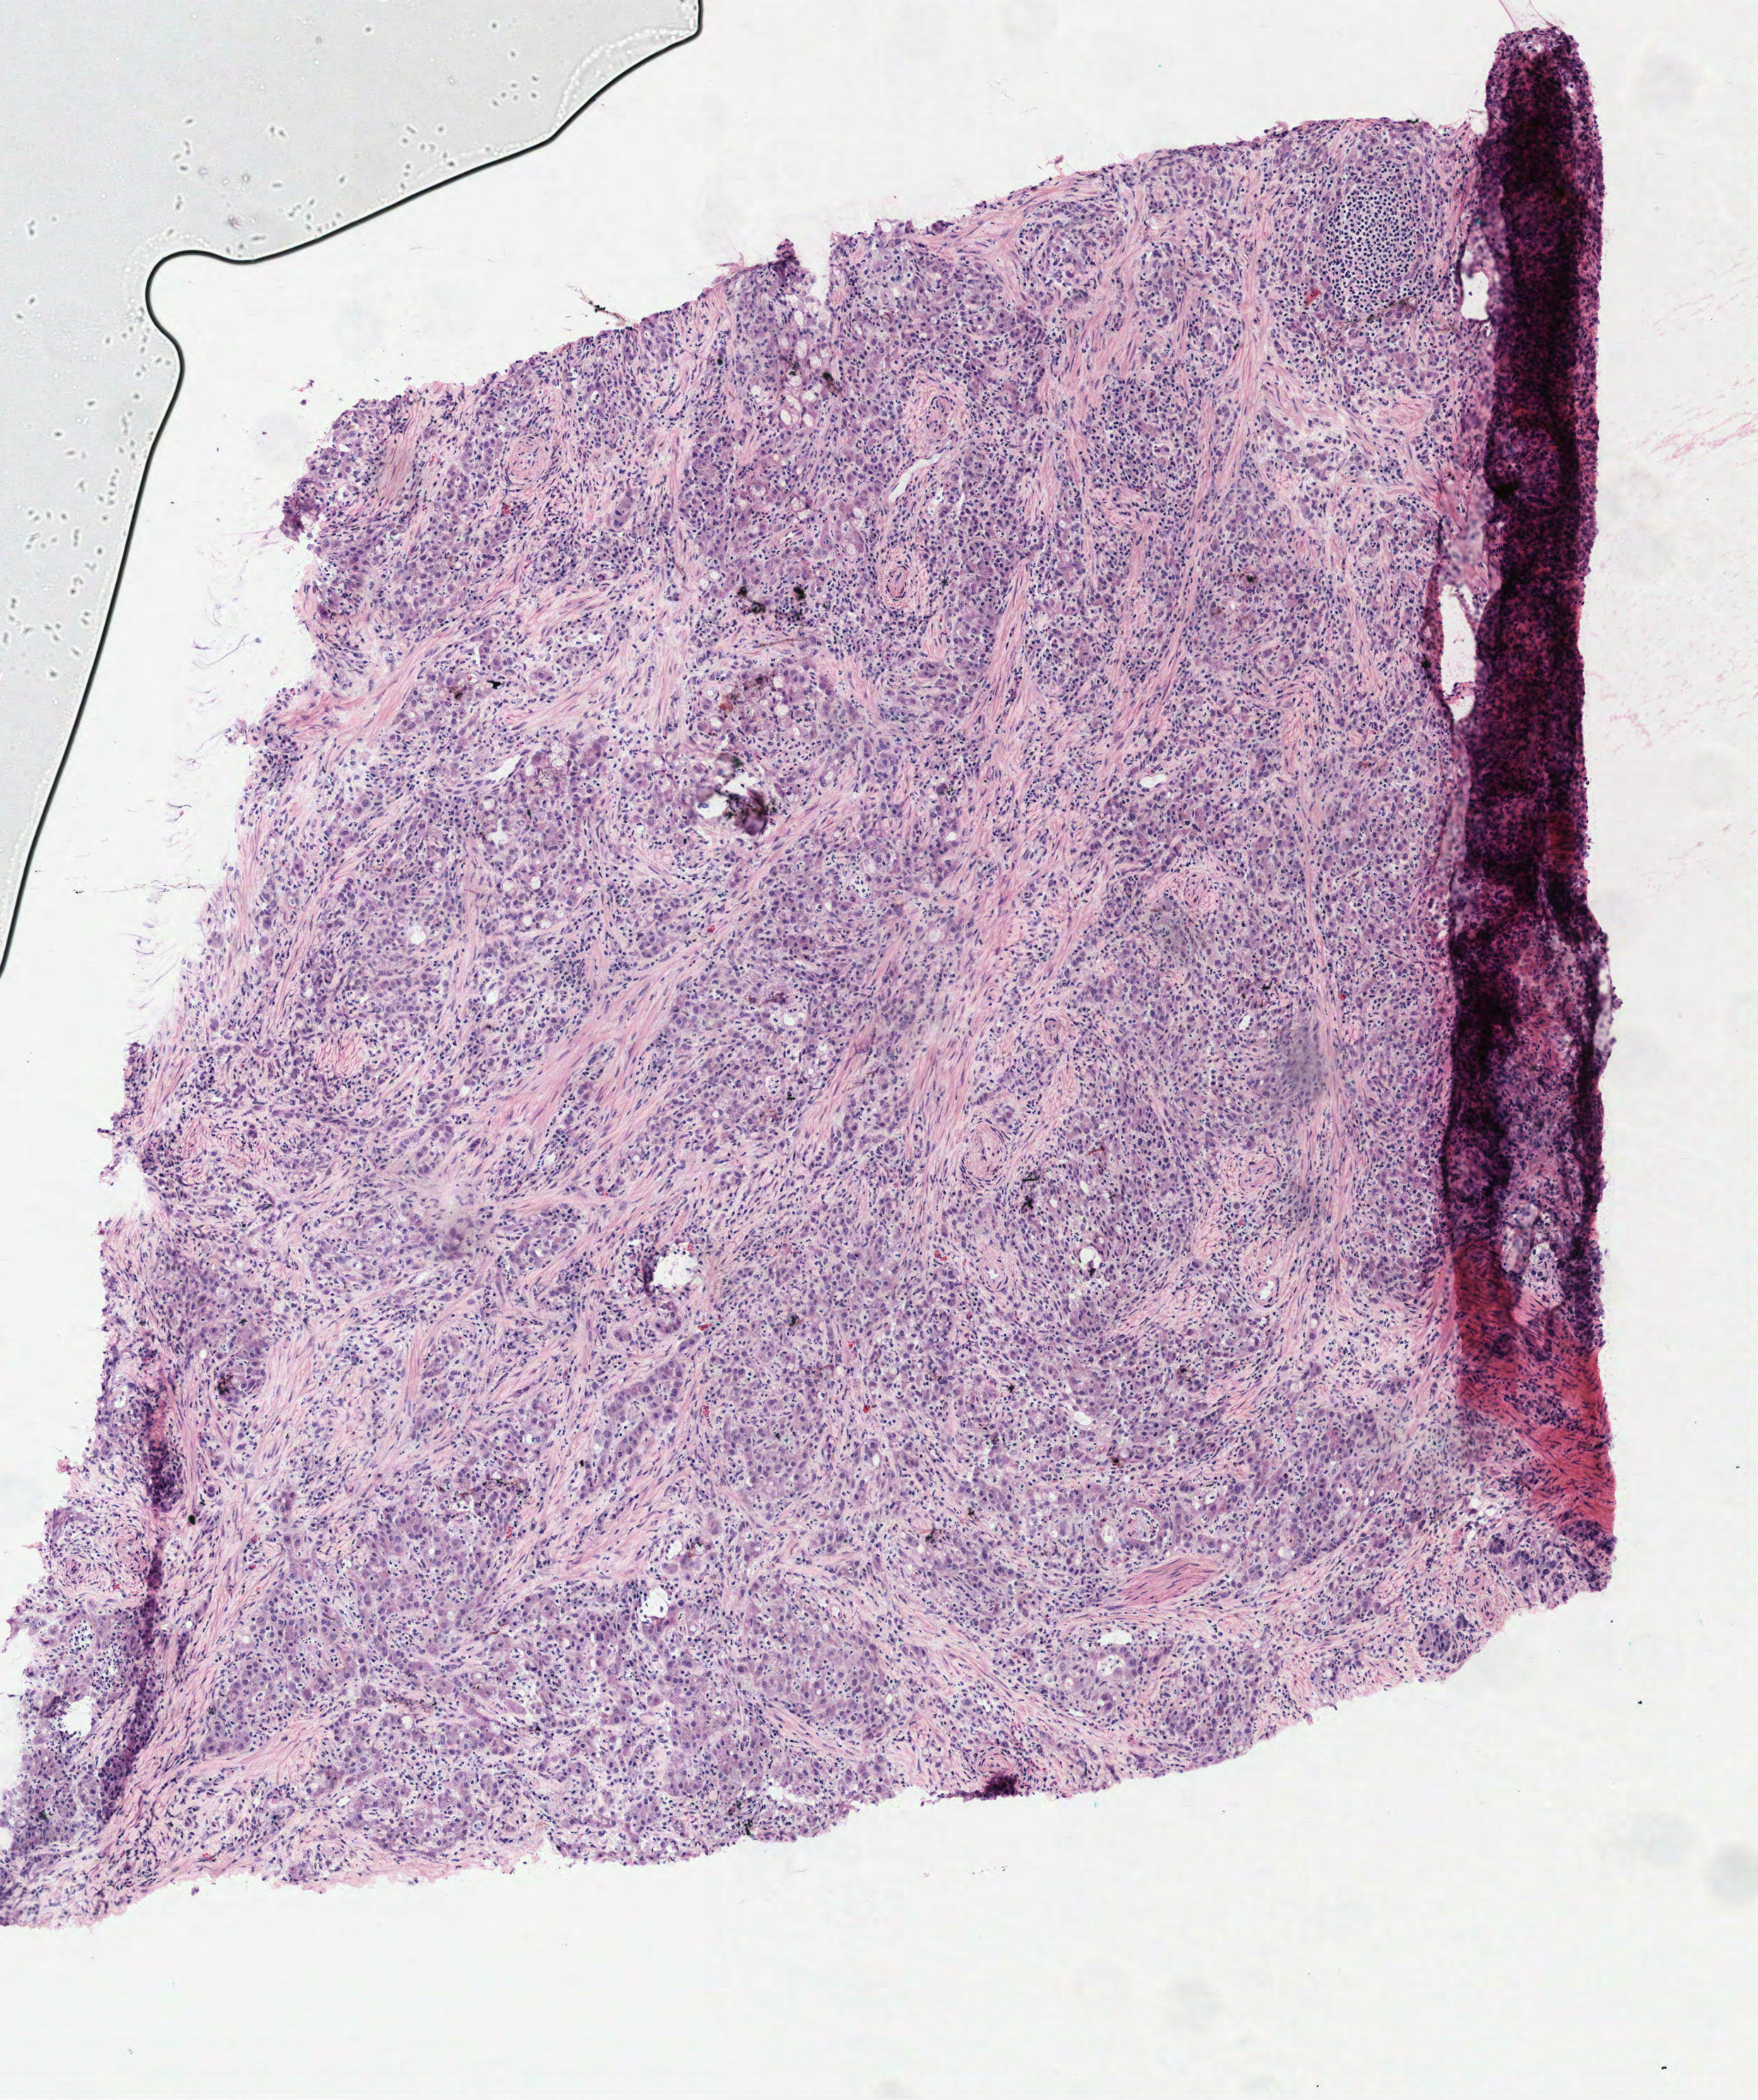
Whole-slide histology image, H&E, low-resolution overview of the scanned area, about 2.5 x 3.0 mm (from a 40x scan), frozen section, primary tumour sample from the stomach. Female patient; age at initial diagnosis 66 years. Histologic grade: G2 (moderately differentiated). Pathologist review of this section (percent, as recorded): tumour cells 100%, tumour nuclei 63%, normal cells 0%, stromal cells 0%, necrosis 0%. Inflammatory infiltration, as recorded: lymphocyte infiltration 15%, monocyte infiltration 0%, neutrophil infiltration 15%.
Lymph nodes positive (case pathology): 4 of 14 examined. AJCC pathologic stage: IIB (7th edition). Pathologic diagnosis: Adenocarcinoma, intestinal type.